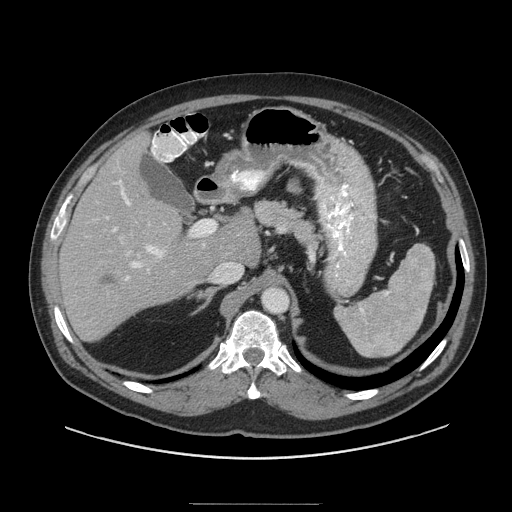
Contrast-enhanced abdominal CT (liver protocol), one axial slice; slice 60 of 91 in the series (ordered by position); reconstruction kernel STANDARD; soft-tissue window (W 400 / L 40 HU); 2.5 mm slice thickness; 512 × 512 image matrix, field of view 440 × 440 mm. Case-level facts recorded for this patient, not image findings: diagnosis: hepatocellular carcinoma (patient treated with transarterial chemoembolisation; whether this scan precedes or follows treatment is not stated here); TNM stage (as recorded): Stage-I; Child-Pugh class: A.
Outlined on this slice (semi-automatic segmentation, software-assisted and operator-edited):
- liver parenchyma outside the tumour (the mass and vessels are separate outlines, so this box may not span the whole liver): bounding box (x1, y1, x2, y2) in pixels: (56, 132, 258, 340)
- mass: (93, 270, 124, 293)
- liver vessels: (106, 180, 241, 281)